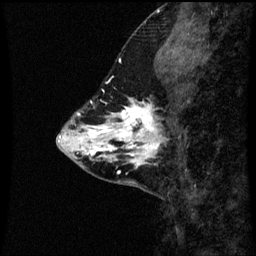
Breast MRI (dynamic contrast-enhanced), one sagittal slice. Slice 19 of 60 in the series (ordered by position). Dynamic contrast-enhanced series, image 2 of 3 at this slice position (ordered by acquisition). 1.5 T. TE 4.2 ms, TR 8.9 ms. 2 mm slice thickness. 256 × 256 image matrix. Female patient, age 43 years. From the clinical record (not read from this slice): setting: breast cancer imaged before/during neoadjuvant chemotherapy; receptor status: HR-positive, HER2-negative.
Annotated regions visible in this slice (semi-automatic segmentation, software-assisted and operator-edited):
- analysis volume of interest (the breast-tissue region the enhancement analysis was run in; not a lesion): bounding box (x1, y1, x2, y2) in pixels: (110, 100, 164, 163)
- tumour enhancement mask (voxels above the 70 % enhancement threshold inside the analysis volume of interest): (110, 100, 163, 163)